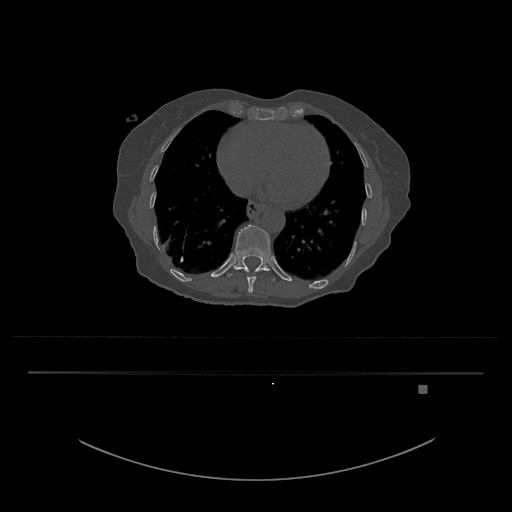
CT including the spine, one axial slice. Position 684 of 797 along the scan axis. Reconstruction kernel Br40s/3. 120 kVp. Bone window (W 1800 / L 400 HU). 0.5 mm slice thickness. 512 × 512 image matrix, field of view 500 × 500 mm. Female patient, age 57 years. From the clinical record (not read from this slice): primary cancer: cervical.
Structures marked on this image (semi-automatically segmented with operator editing):
- T10 vertebra: bounding box <244,270,262,293> (left, top, right, bottom; pixels)
- T11 vertebra: <227,225,275,281>